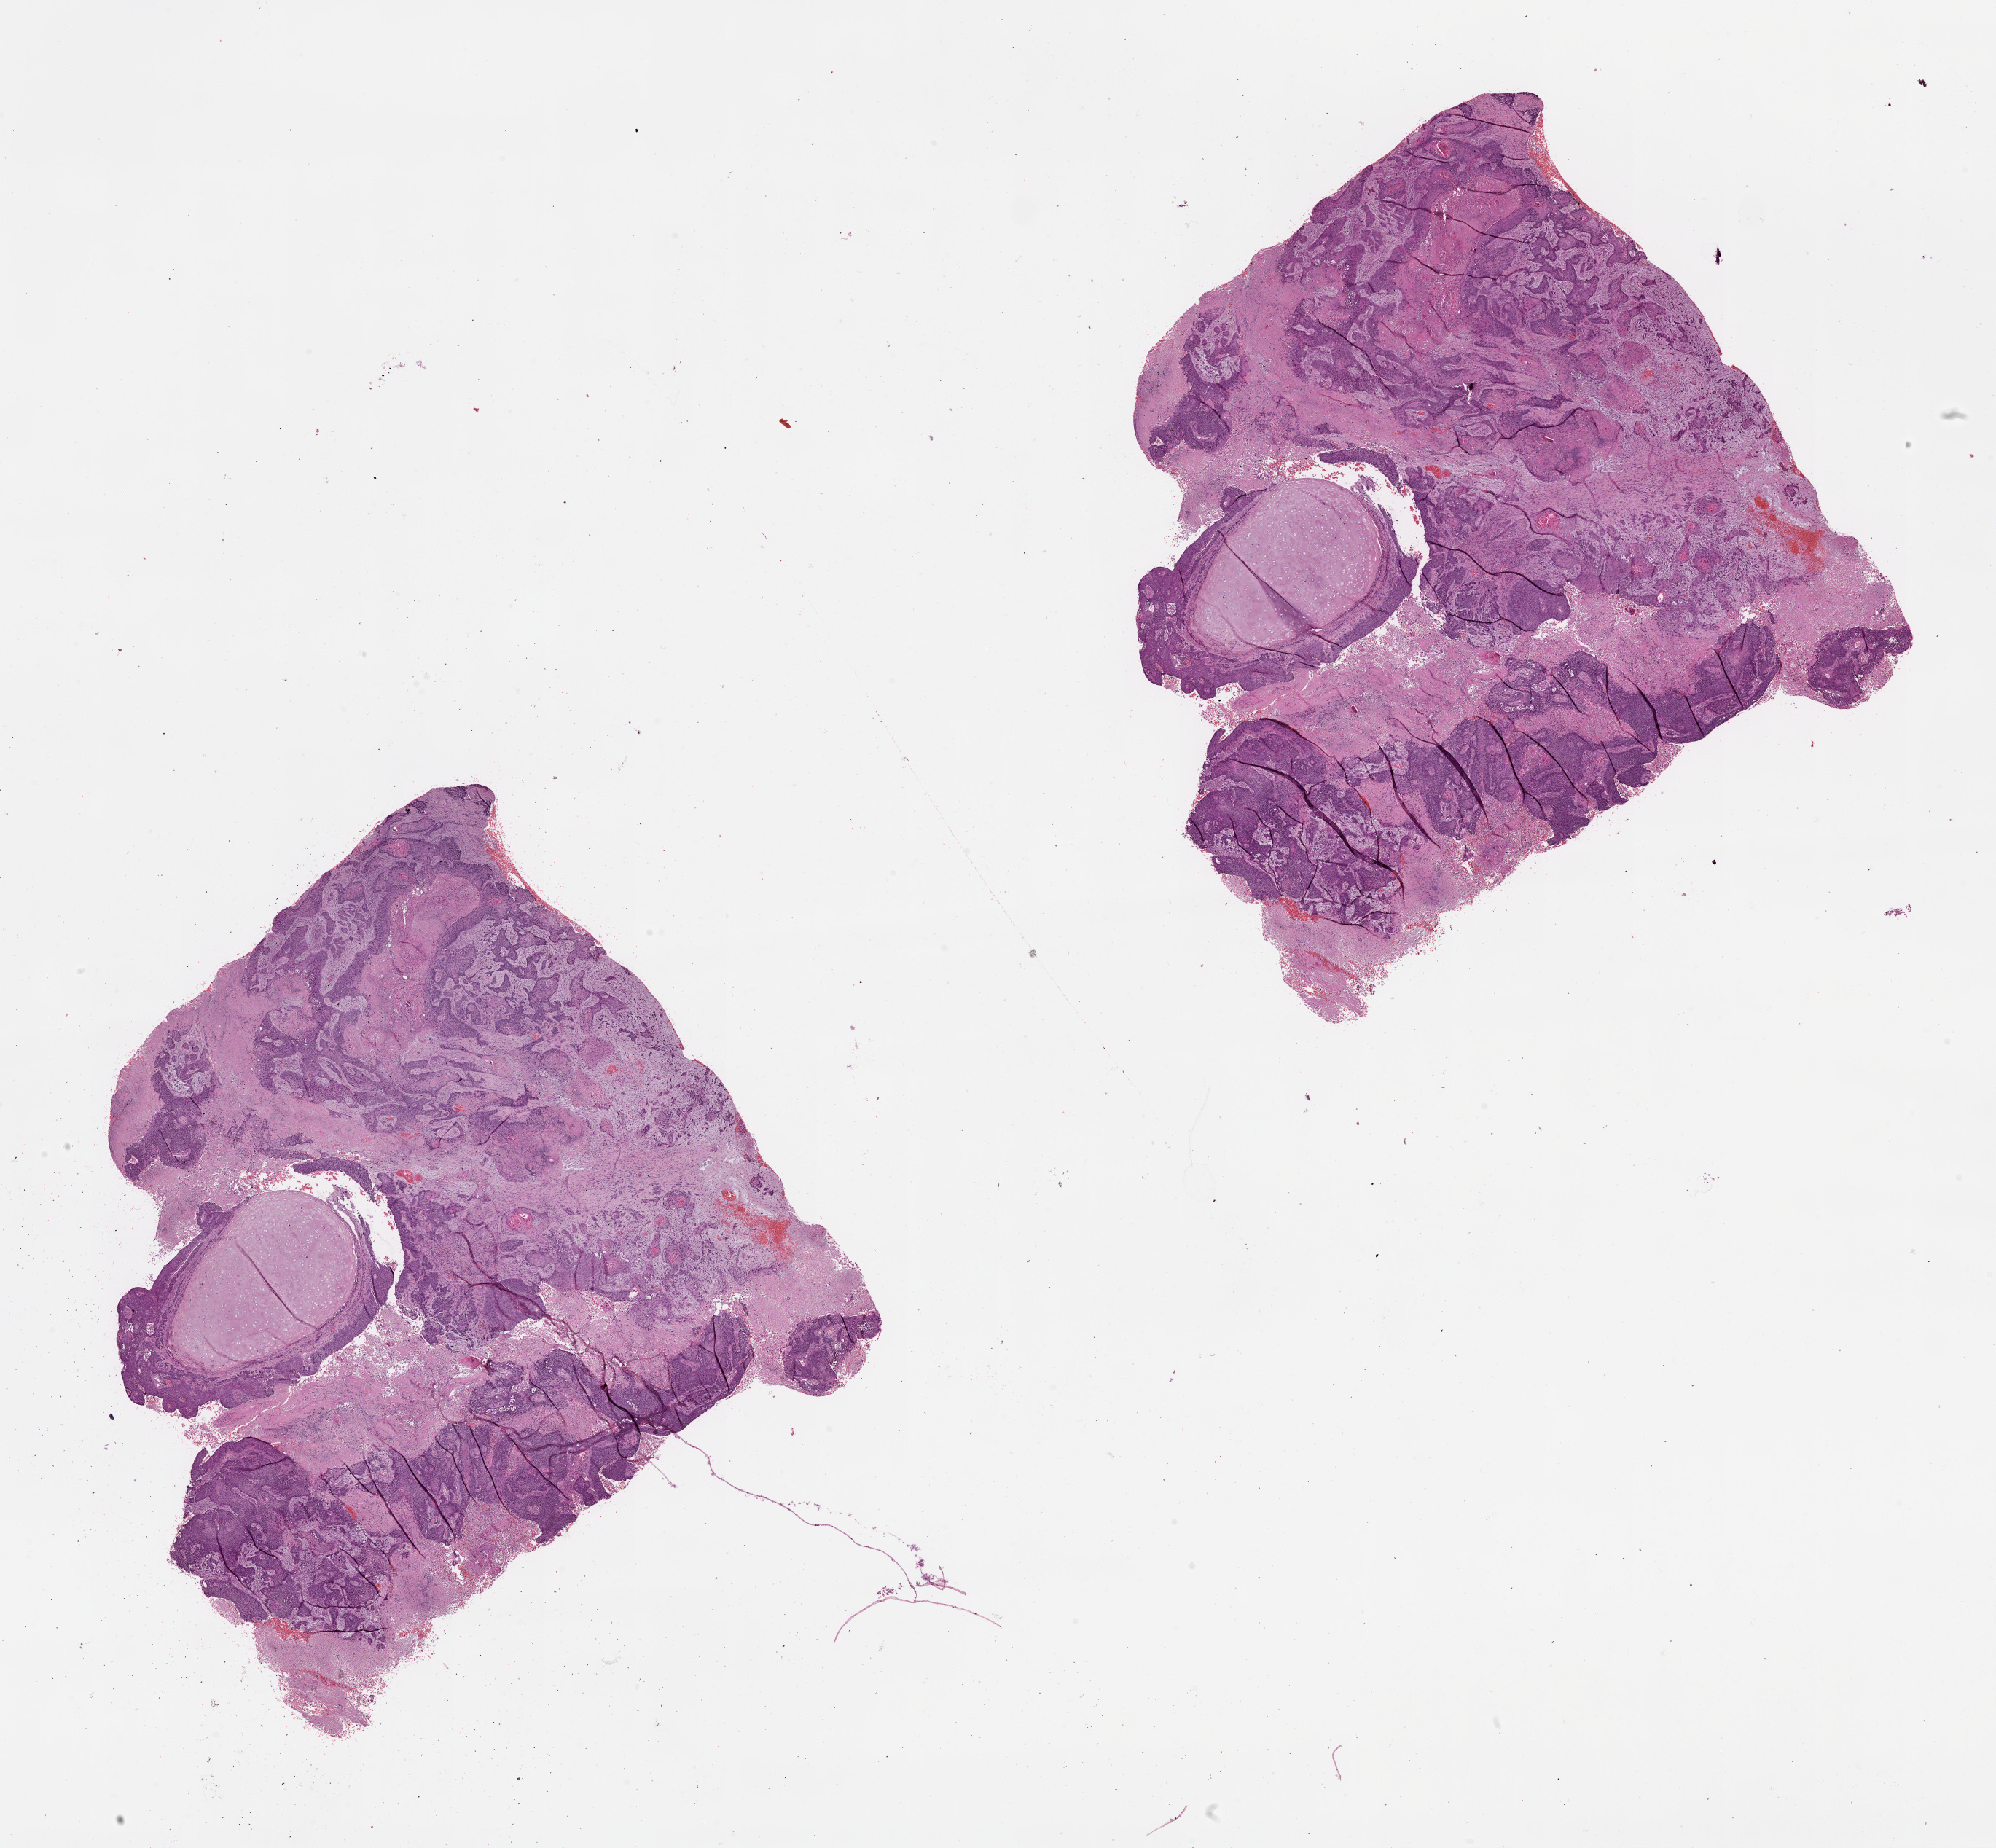
H&E whole-slide image, whole scanned area (about 22.0 x 20.4 mm, from a 20x scan) shown as a low-resolution overview. Lung, tumour tissue. Patient: male, age 59 years.
Patient diagnosis (cohort enrolment): squamous cell carcinoma (lung).